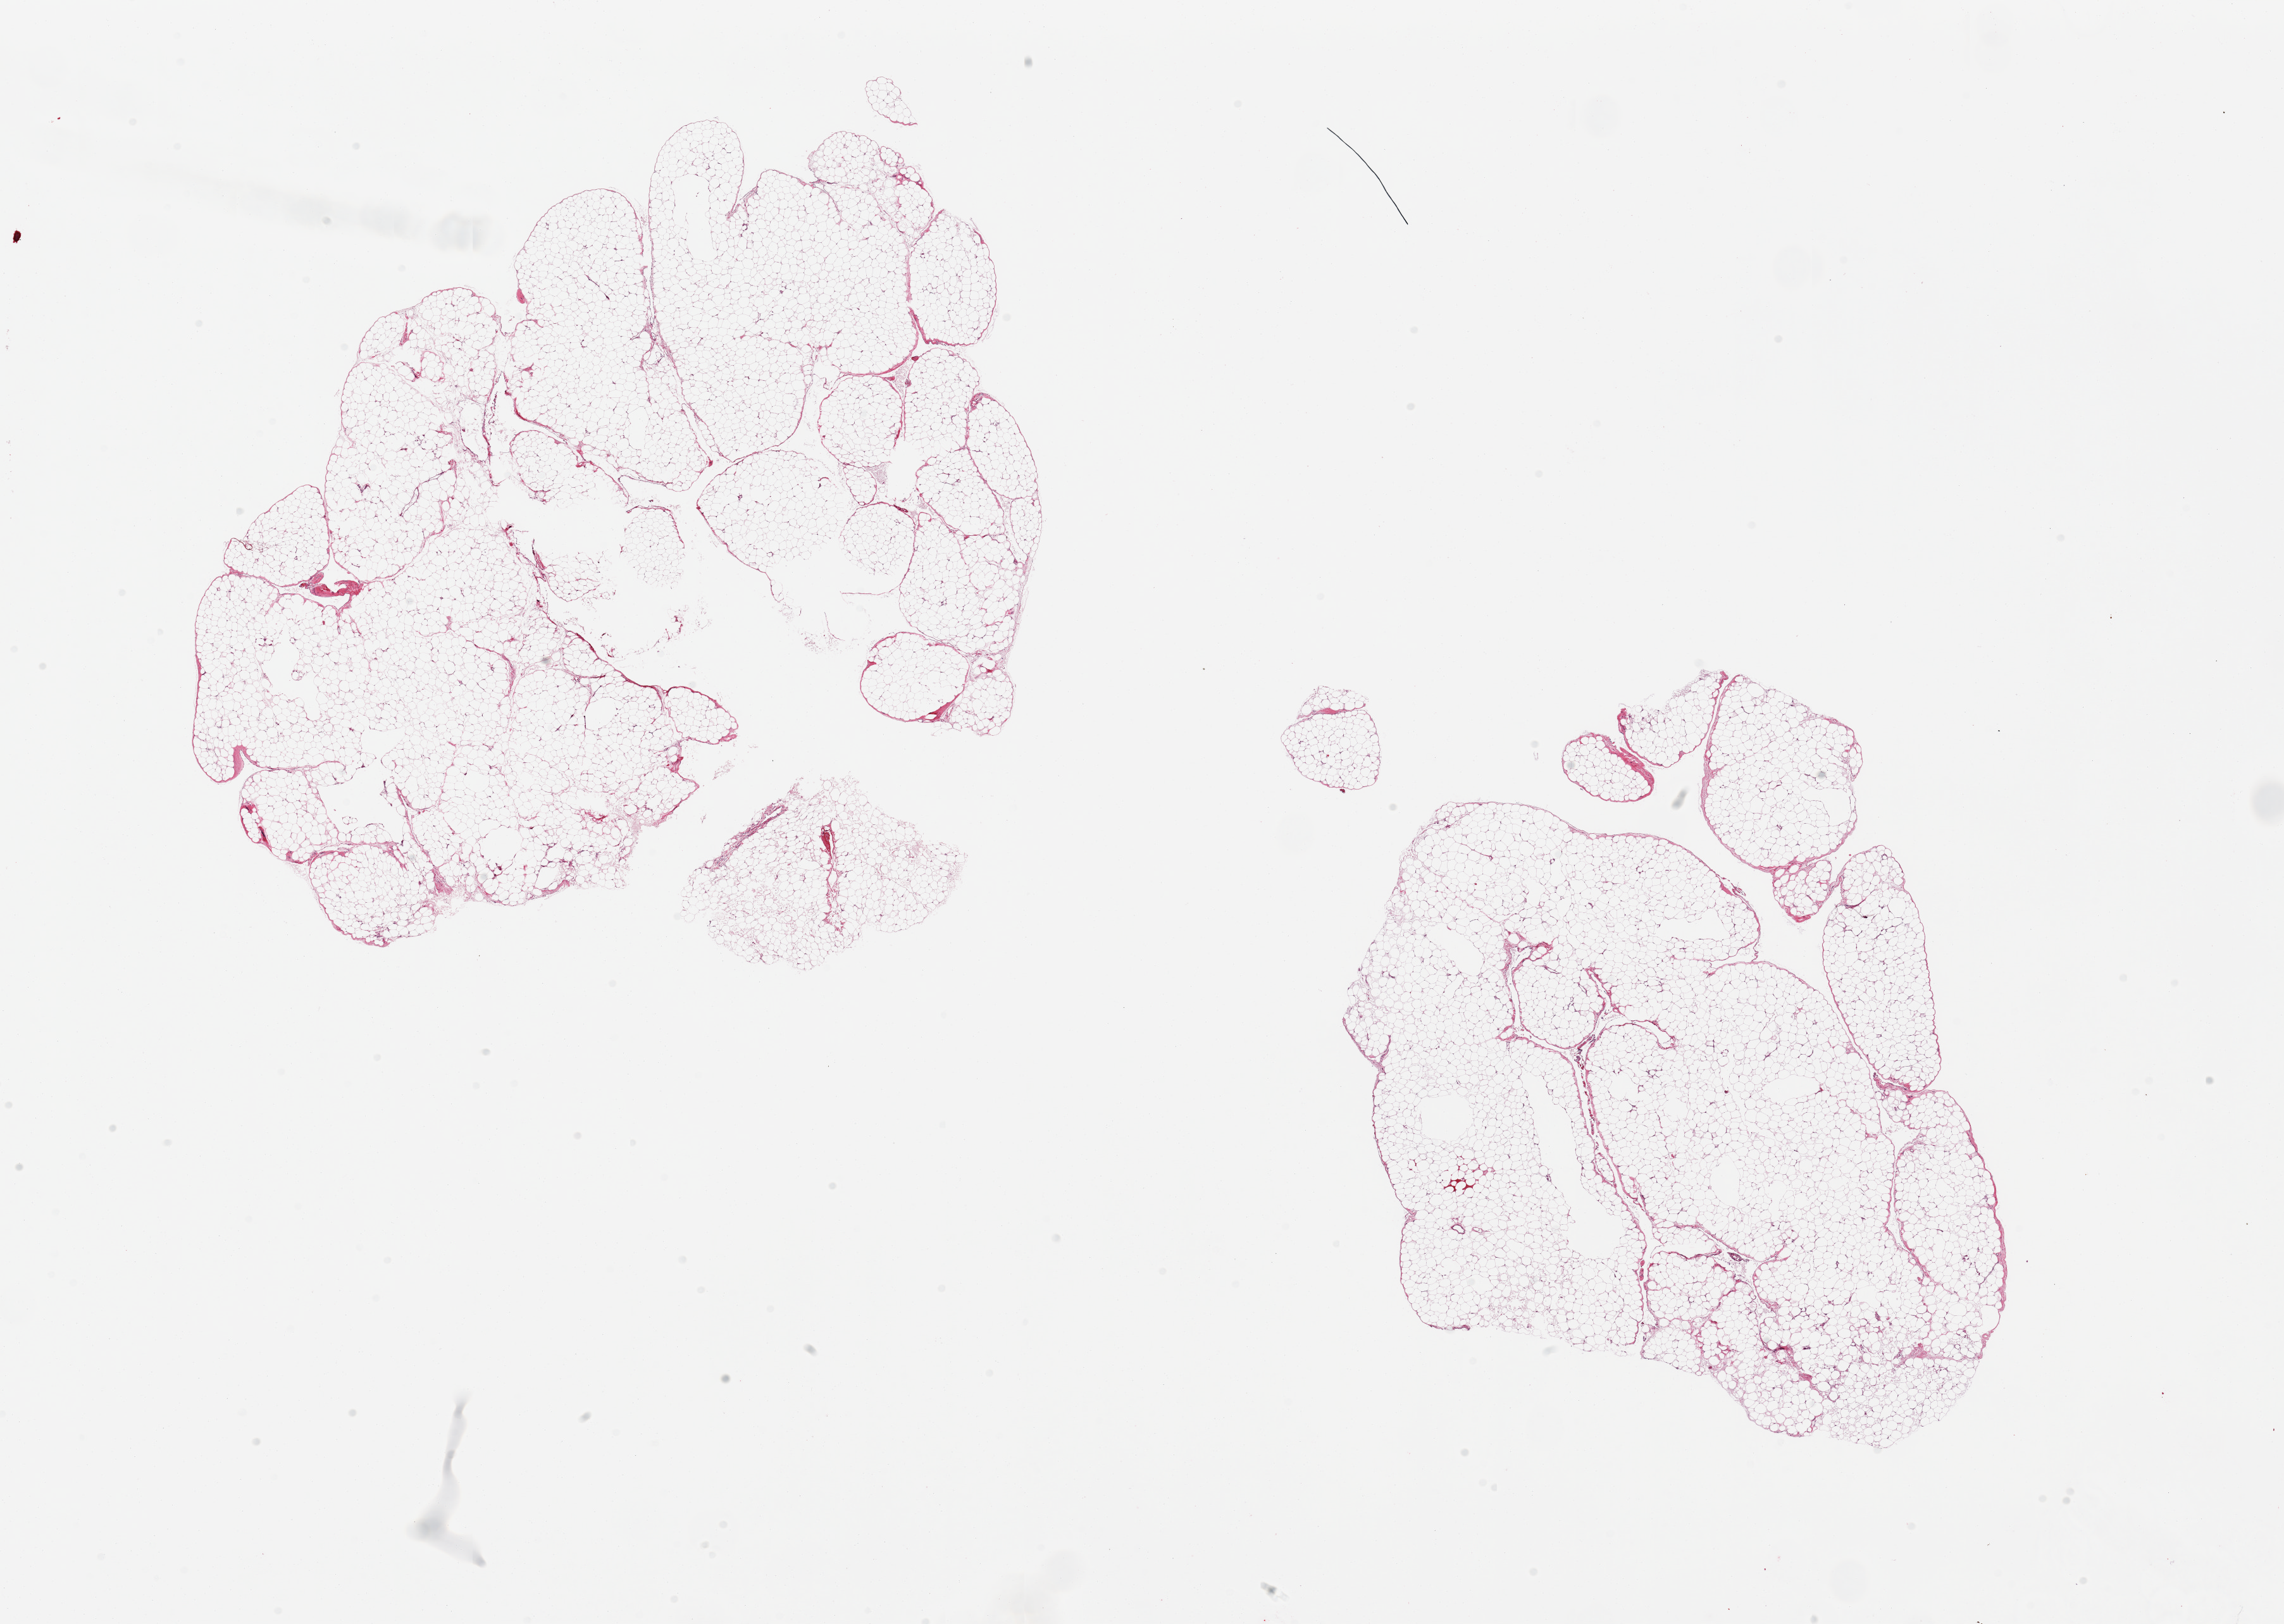
Whole-slide image, haematoxylin and eosin stain, brightfield — a low-resolution overview of the entire scanned area, about 28.5 x 20.3 mm (acquisition: 20x scan); PAXgene-fixed paraffin-embedded (PFPE) section; sampled site (target tissue): omentum; tissue donor sample. Donor: female.
Reviewer comment on this tissue sample: 2 pieces.